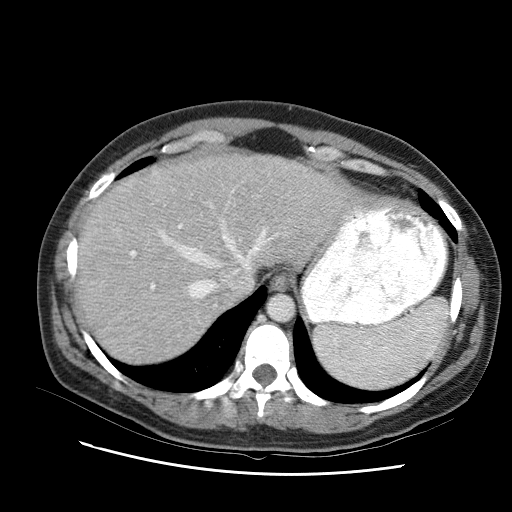
Contrast-enhanced abdominal CT (liver protocol), one axial slice. Slice 75 of 95 in the series (ordered by position). Reconstruction kernel STANDARD. 120 kVp. One of 2 acquisitions stored at this slice position. Soft-tissue window (W 400 / L 40 HU). 2.5 mm slice thickness. 512 × 512 image matrix. From the clinical record (not read from this slice): diagnosis: hepatocellular carcinoma (patient treated with transarterial chemoembolisation; whether this scan precedes or follows treatment is not stated here); TNM stage (as recorded): Stage-I; Child-Pugh class: B; tumour differentiation: moderately differentiated; tumour nodularity: uninodular.
Structures marked on this image (semi-automatic segmentation, software-assisted and operator-edited):
- liver parenchyma outside the tumour (the mass and vessels are separate outlines, so this box may not span the whole liver): bounding box [x1, y1, x2, y2] px = [76, 150, 353, 344]
- liver vessels: [113, 192, 238, 296]